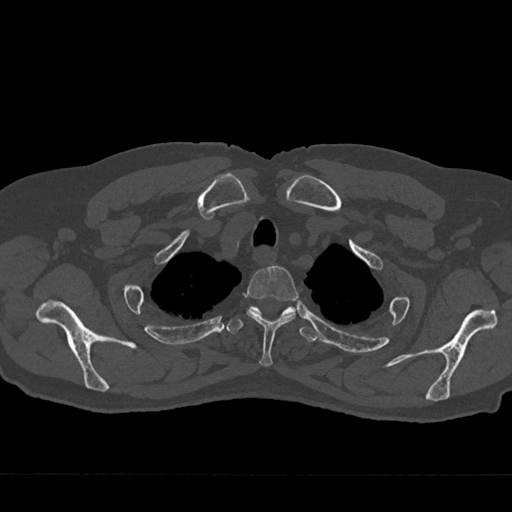
CT including the spine, one axial slice. Slice 598 of 797 in the series (ordered by position). Reconstruction kernel Br40s/3. 120 kVp. Bone window (W 1800 / L 400 HU). 0.5 mm slice thickness. 512 × 512 image matrix. Patient: male, 75 years. Case-level facts recorded for this patient, not image findings: primary cancer: renal; vertebrae with lytic lesions (as recorded): T4.
Annotated regions visible in this slice (semi-automatically segmented with operator editing):
- T2 vertebra: bounding box <244,265,299,367> (left, top, right, bottom; pixels)
- T3 vertebra: <226,306,317,342>